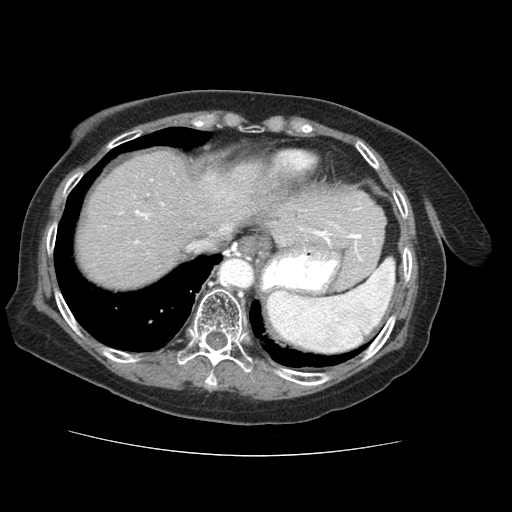
Contrast-enhanced abdominal CT (liver protocol), one axial slice. Position 54 of 73 along the scan axis. Reconstruction kernel STANDARD. 120 kVp. Soft-tissue window (W 400 / L 40 HU). 512 × 512 image matrix. Case-level facts recorded for this patient, not image findings: diagnosis: hepatocellular carcinoma (patient treated with transarterial chemoembolisation; whether this scan precedes or follows treatment is not stated here); TNM stage (as recorded): Stage-IVB; Child-Pugh class: A; tumour differentiation: well differentiated.
Annotated regions visible in this slice (semi-automatic segmentation, software-assisted and operator-edited):
- abdominal aorta: bounding box (x1, y1, x2, y2) in pixels: (219, 259, 252, 287)
- liver parenchyma outside the tumour (the mass and vessels are separate outlines, so this box may not span the whole liver): (78, 150, 266, 288)
- liver vessels: (120, 180, 230, 243)